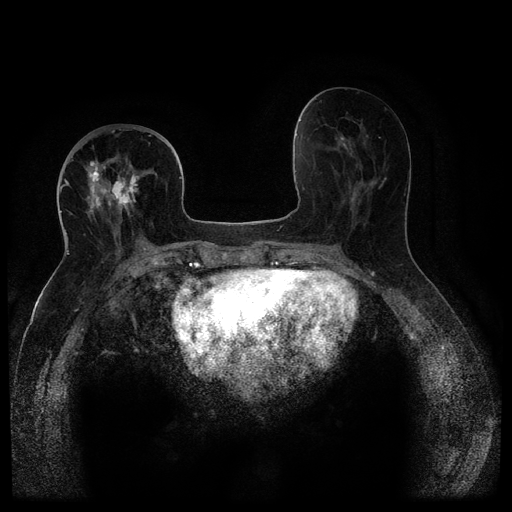
Breast MRI (dynamic contrast-enhanced, multi-phase), one axial slice; slice 48 of 116 in the series (ordered by position); dynamic contrast-enhanced series, time point 2 of 5 at this slice position (early post-contrast); 1.5 T; TE 2.6 ms, TR 5.4 ms; 2 mm slice thickness; 512 × 512 image matrix, field of view 340 × 340 mm. Patient: female, 68 years.
Structures marked on this image (semi-automatic segmentation, software-assisted and operator-edited):
- breast lesion (labelled 'tumour' in the annotation; benign lesions carry a separate 'benign' label): box from (x=110, y=167) to (x=143, y=212) px
- breast lesion (labelled 'tumour' in the annotation; benign lesions carry a separate 'benign' label): (x=86, y=147)–(x=108, y=211)